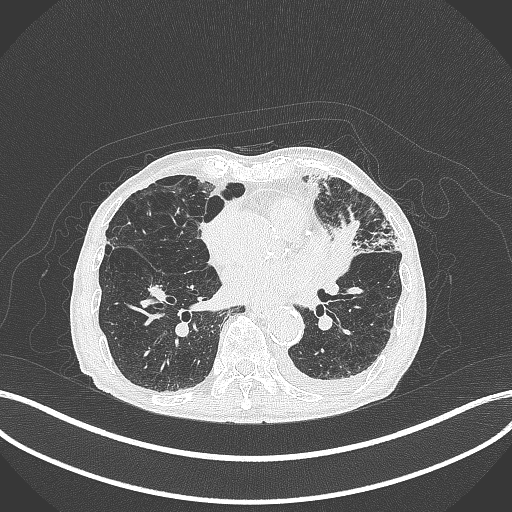
Chest CT, one axial slice; slice 158 of 385 in the series (ordered by position); 120 kVp; lung window (W 1500 / L -600 HU); 1 mm slice thickness; 512 × 512 image matrix, field of view 400 × 400 mm. Male patient, age 90 years or older. Case-level facts recorded for this patient, not image findings: clinical TNM (as recorded): T2b N1 M0.
Outlined on this slice (rectangle marked by the reading radiologist):
- lung tumour (recorded histology: squamous cell carcinoma): bounding box (x1, y1, x2, y2) in pixels: (332, 217, 357, 278)